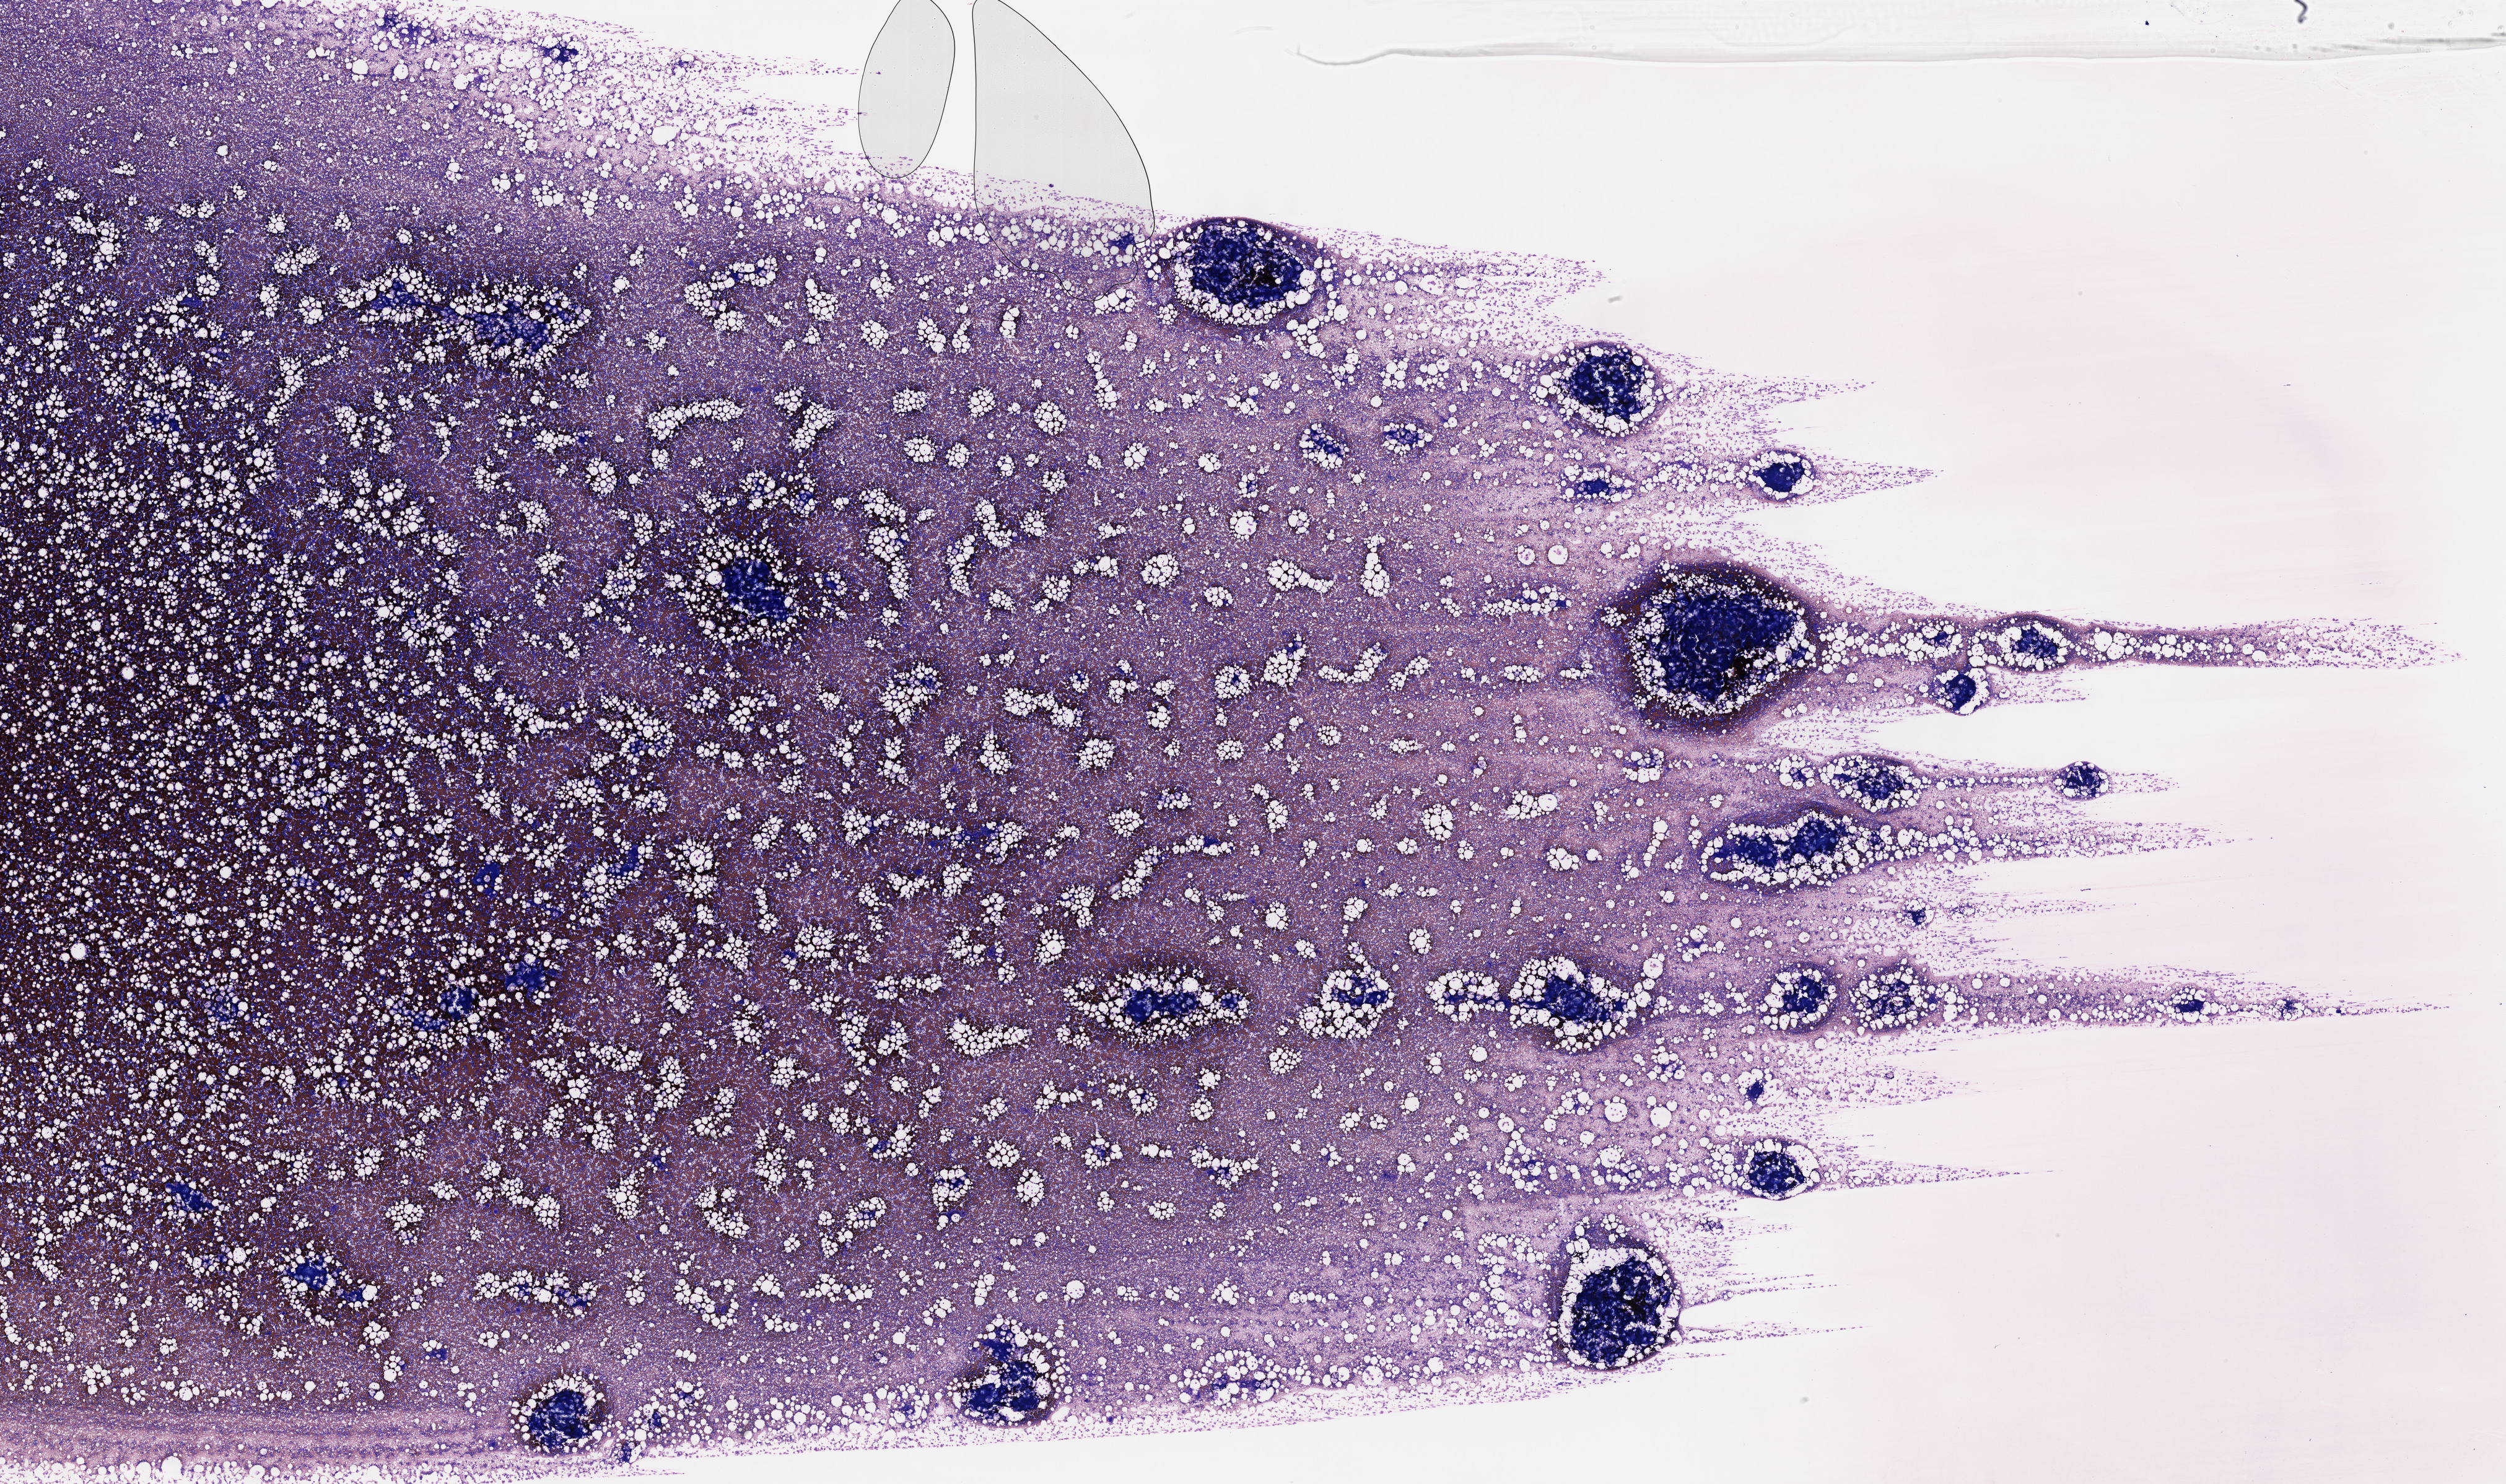
Whole-slide image, Wright–Giemsa stain, a low-resolution overview of the entire scanned area, about 32.7 x 19.4 mm. Specimen: tumor tissue. Site: bone marrow. Female patient, 11 years old.
- diagnosis: Burkitt lymphoma, NOS